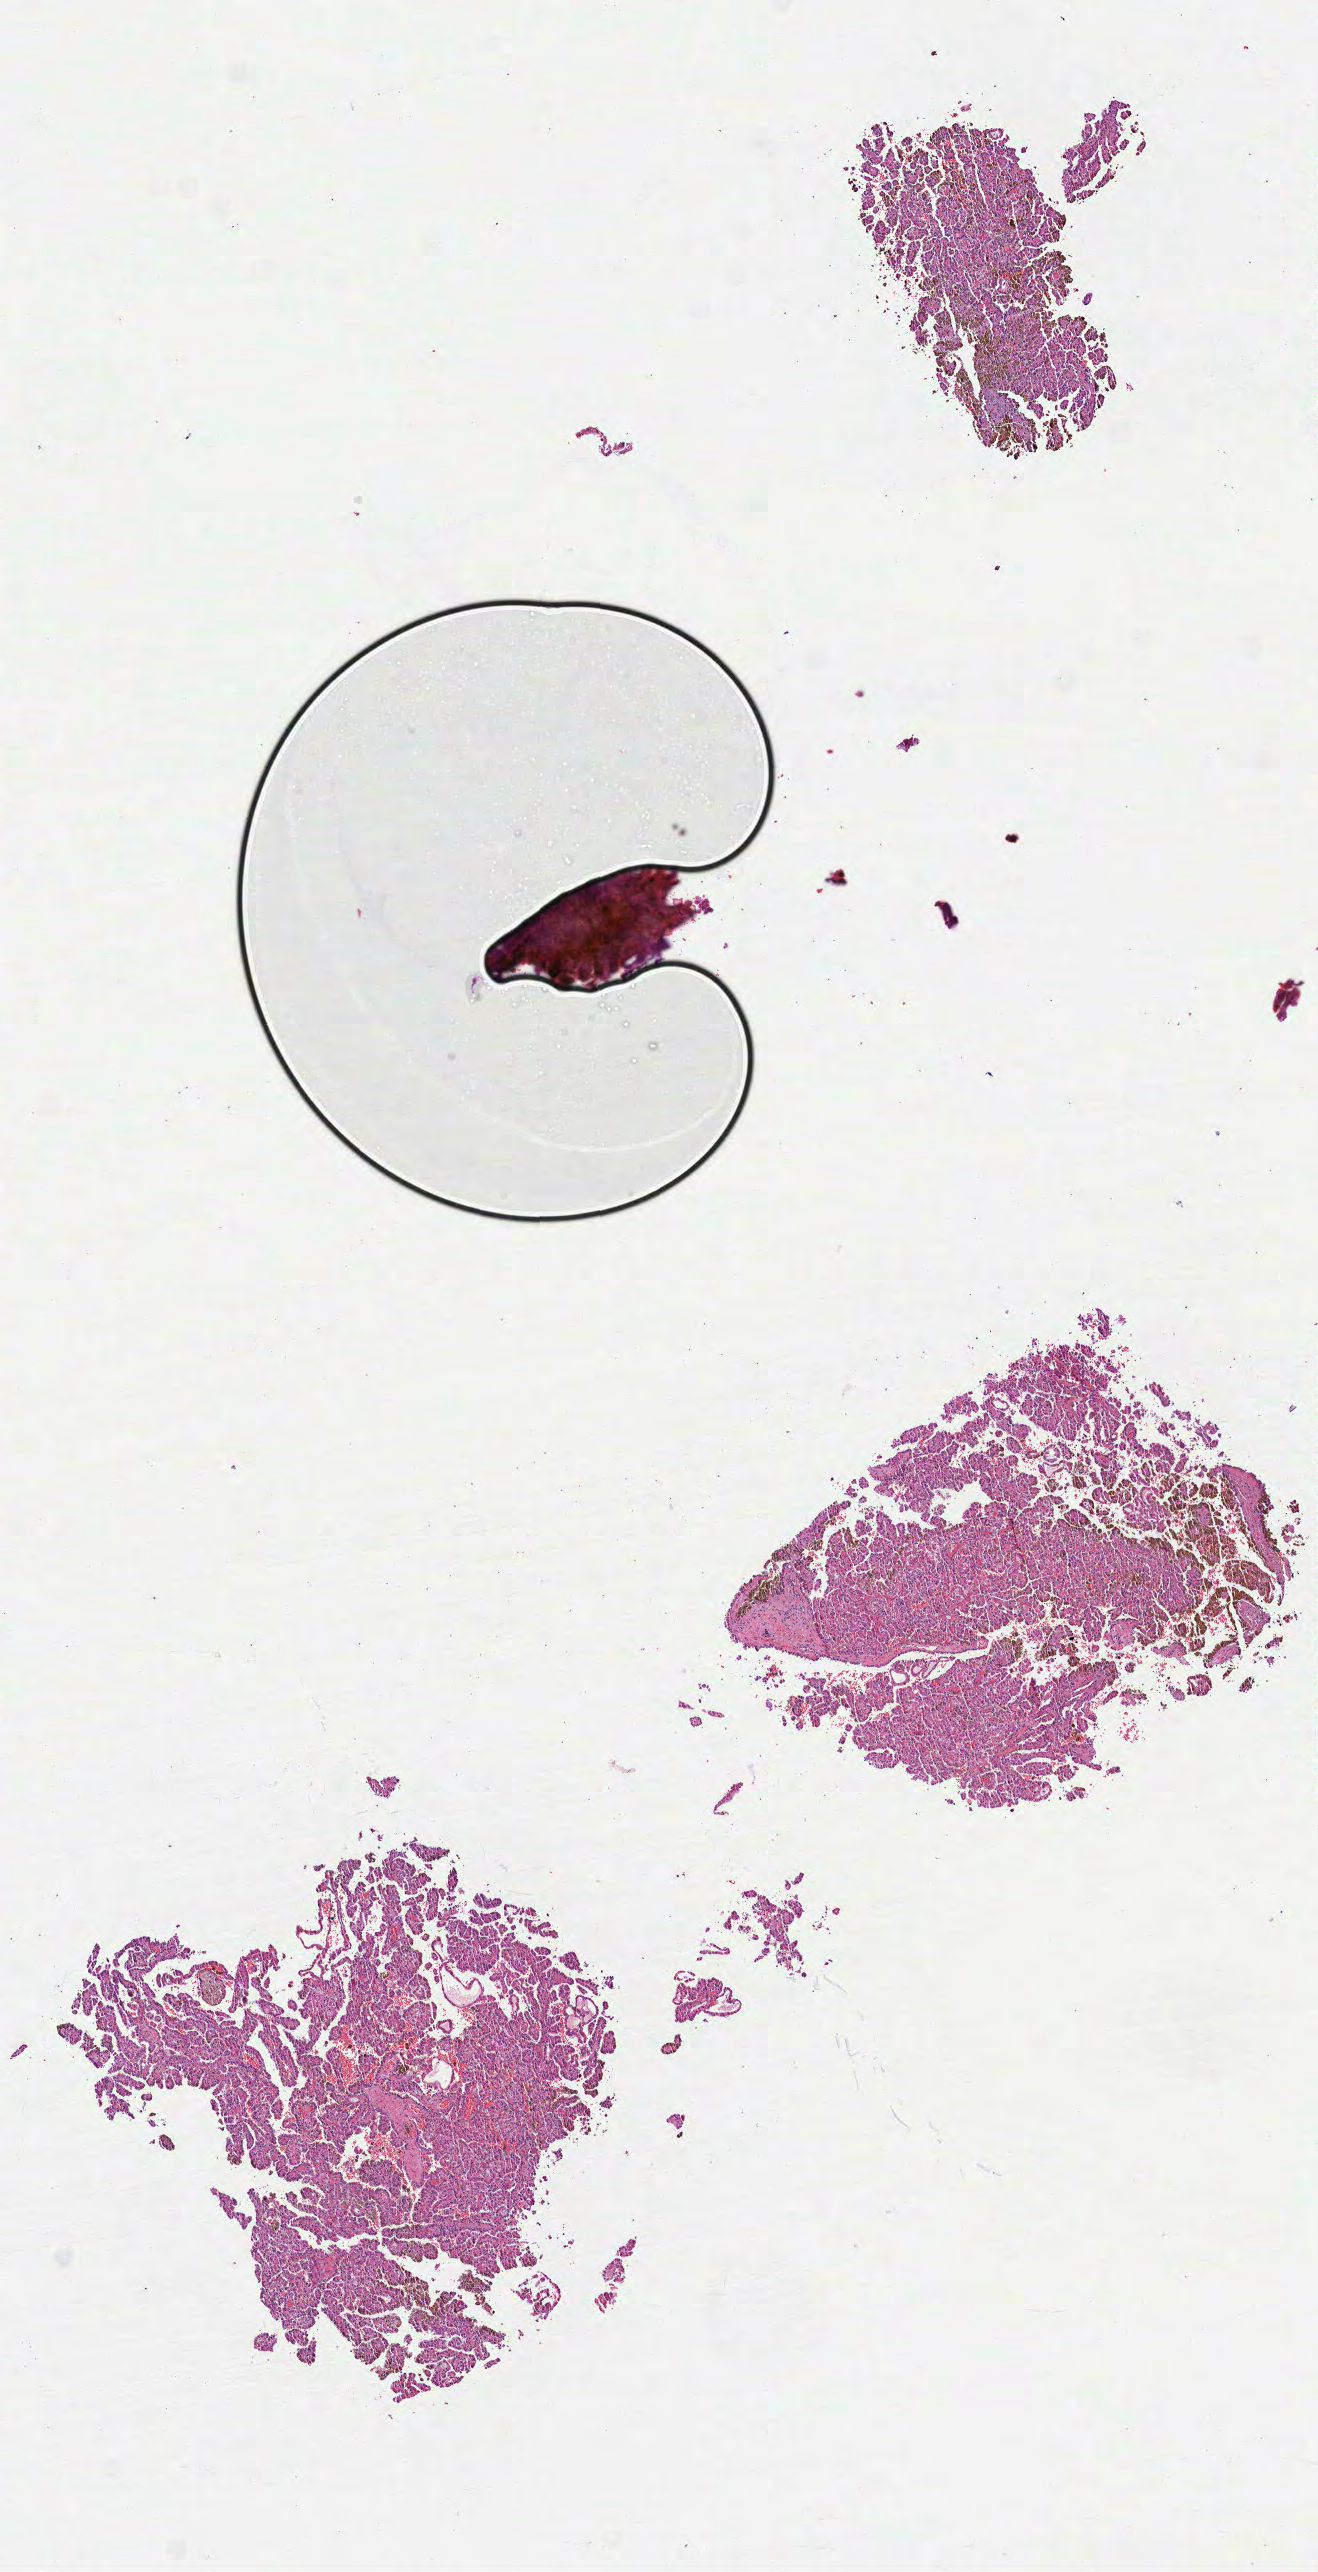
Whole-slide histology image, H&E-stained — a low-resolution overview of the entire scanned area, about 5.3 x 10.4 mm (from a 40x scan). FFPE section. Sample: primary tumour, kidney. Female, age 71 years at initial diagnosis.
Laterality: right. Histologic diagnosis: Papillary adenocarcinoma, NOS.